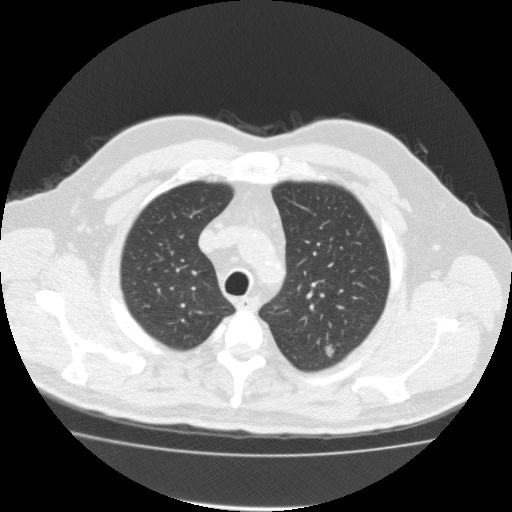
Low-dose screening chest CT, one axial slice. Slice 134 of 161 in the series (ordered by position). 120 kVp. Lung window (W 1500 / L -600 HU). 2 mm slice thickness. 512 × 512 image matrix, field of view 412 × 412 mm.
Outlined on this slice (manually delineated by an expert):
- lesion 1 (tumor, upper lobe of left lung): box from (x=325, y=344) to (x=335, y=358) px